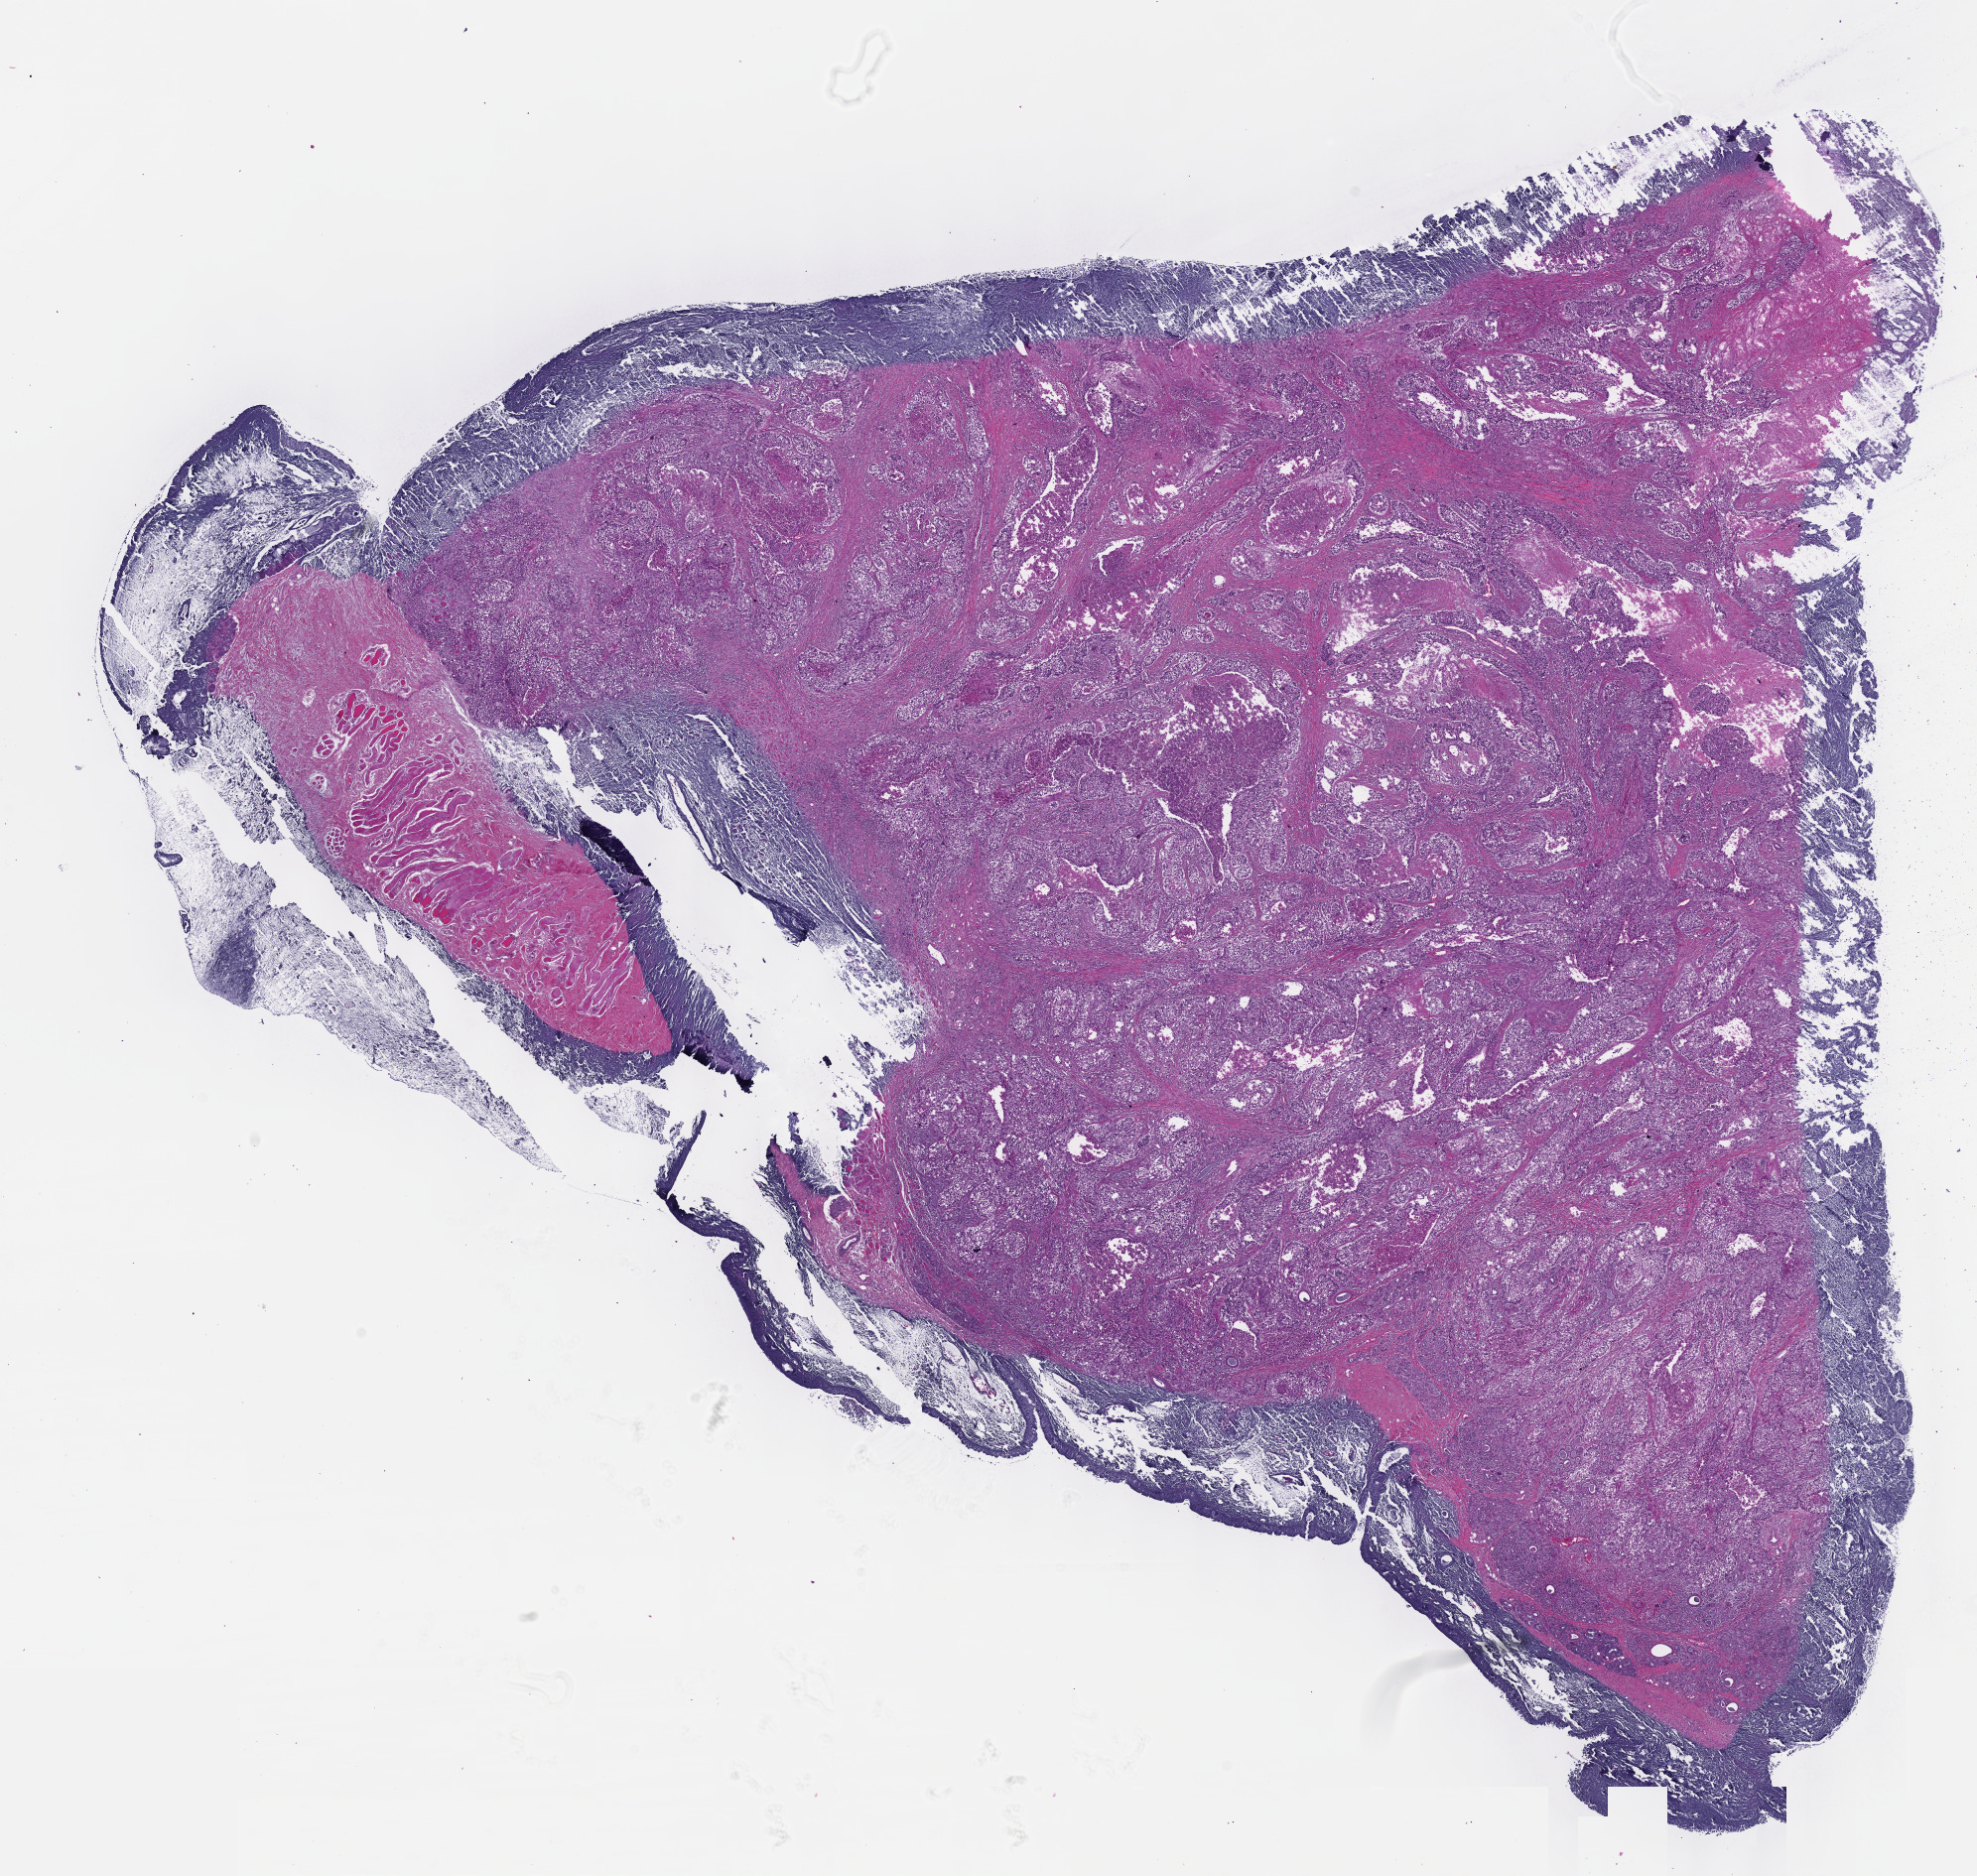
Digitized H&E-stained tissue section (whole slide), shown as a low-resolution overview of the whole scanned area (about 16.1 x 15.3 mm); formalin-fixed paraffin-embedded (FFPE) diagnostic section; primary tumour sample from the head and neck. Male patient; age at initial diagnosis 67 years. Histologic grade: G2 (moderately differentiated).
Pathologic diagnosis: Squamous cell carcinoma, NOS (larynx, NOS). TNM: T3 N2b. AJCC pathologic stage: IVA (7th edition).